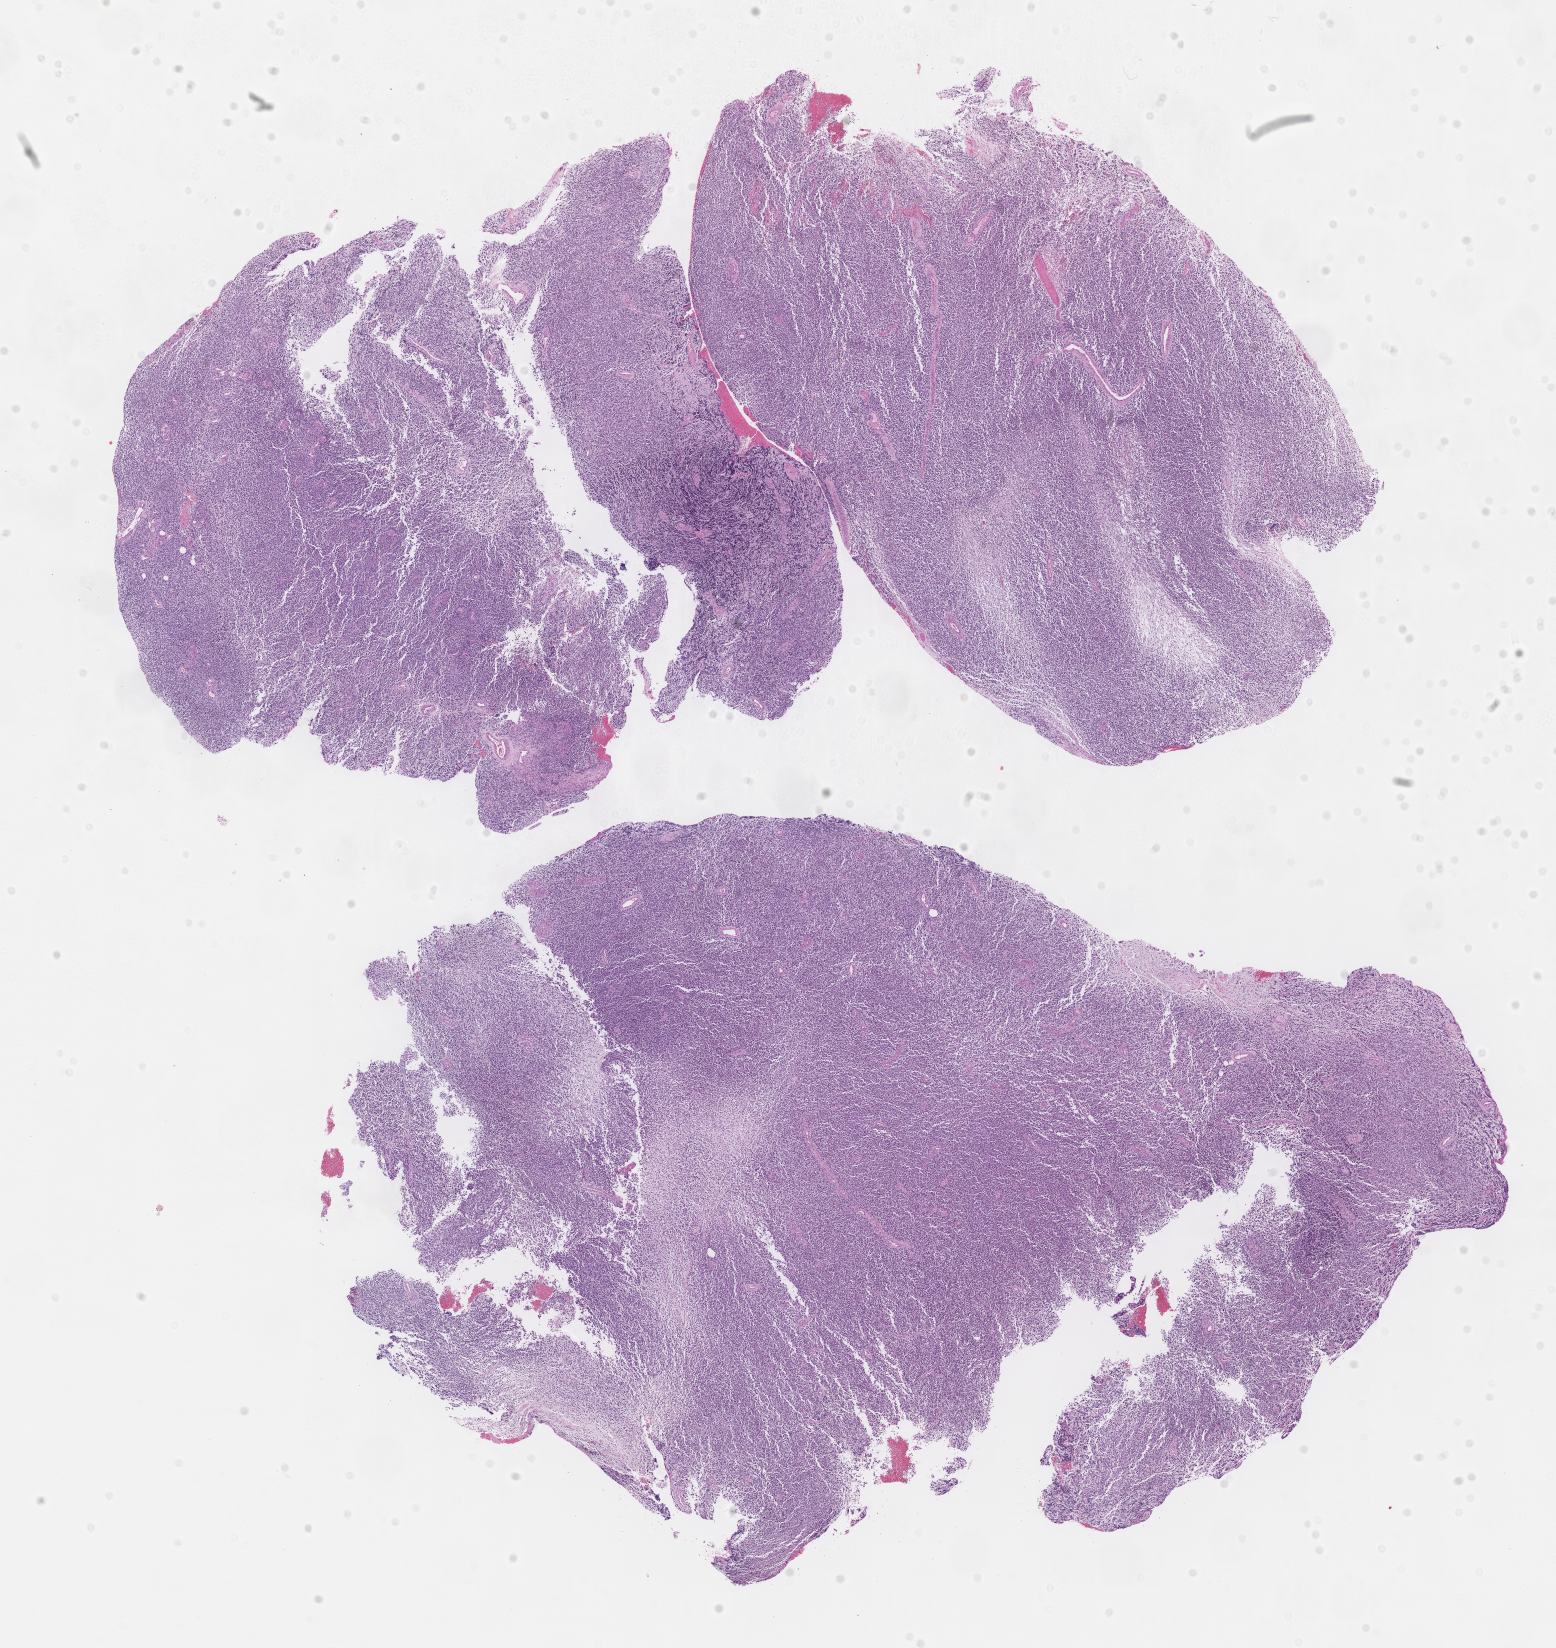
Digitized H&E-stained section of tumor tissue — whole scanned area (about 12.6 x 13.3 mm) shown as a low-resolution overview; formalin-fixed paraffin-embedded section; site: pelvis. Male patient, age at diagnosis 5.2 years.
- stage (as recorded): 3
- diagnosis: rhabdomyosarcoma; histological classification: embryonal rhabdomyosarcoma